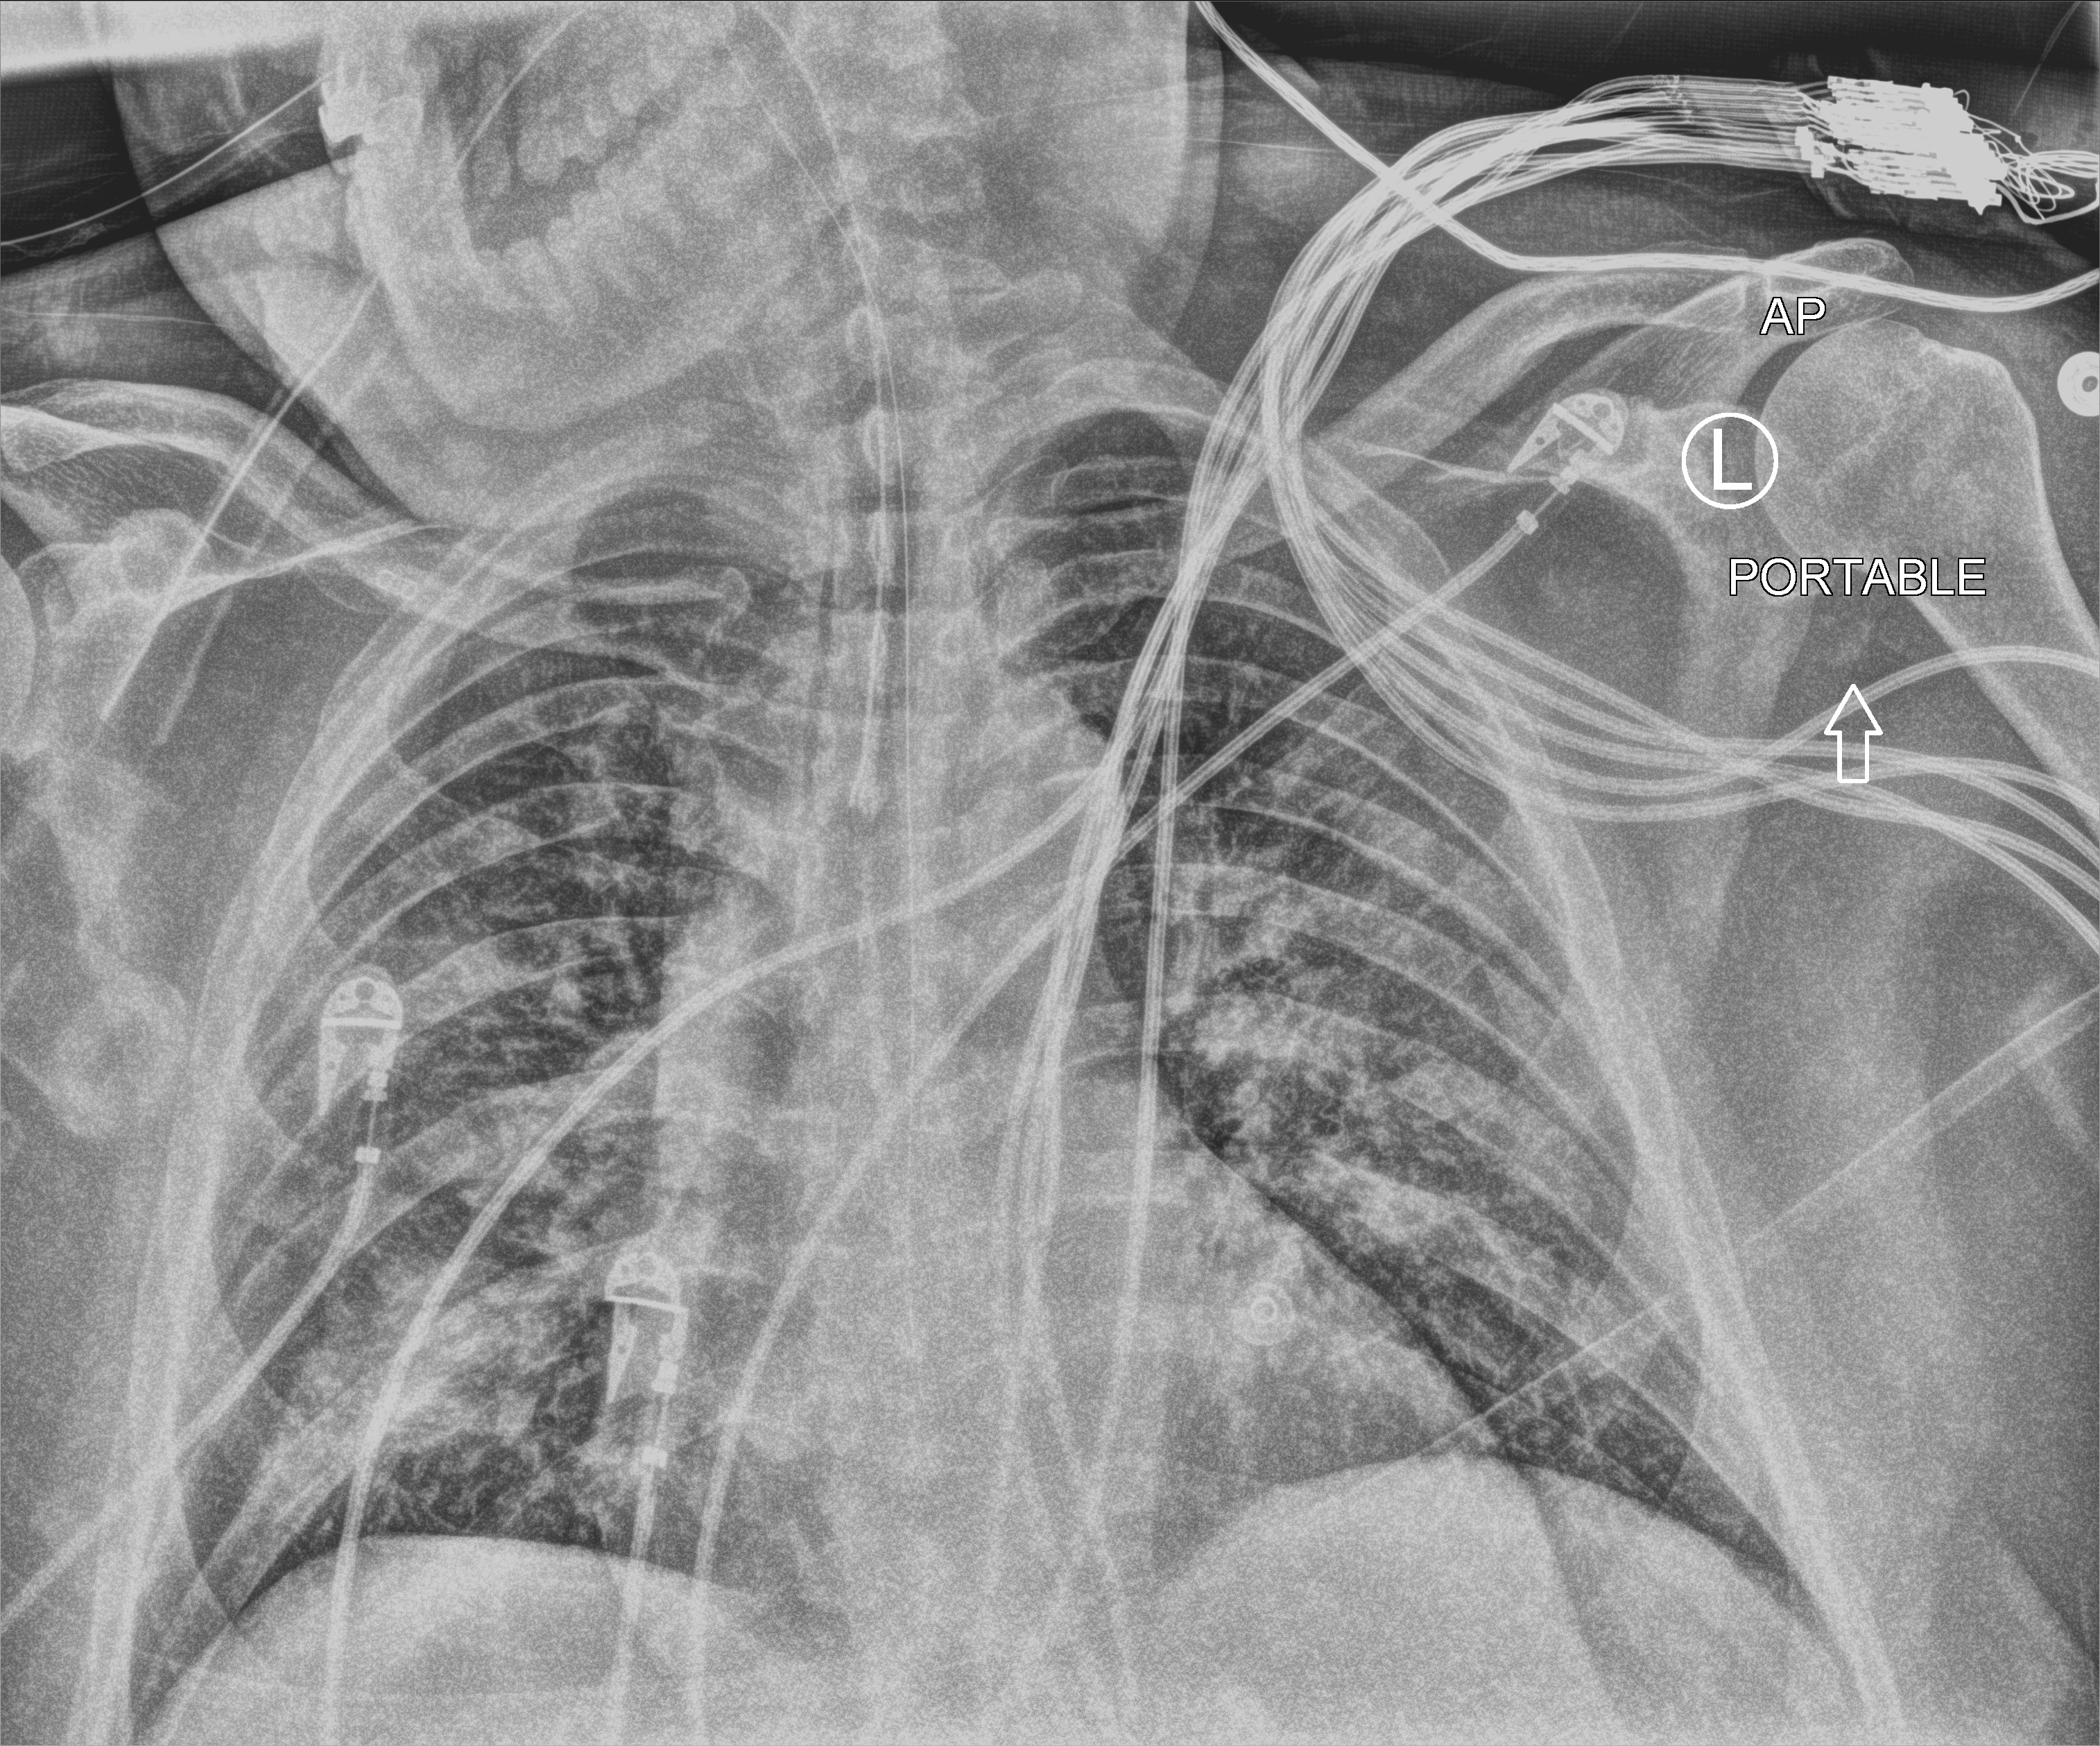
Portable chest radiograph, anteroposterior (AP) projection. Male patient hospitalised with COVID-19, age 60–74 years.
From the hospital-stay record, not from the radiograph (when in the stay this image was taken is not recorded):
- admitted to intensive care during this hospital stay: yes
- mechanically ventilated during this hospital stay: yes